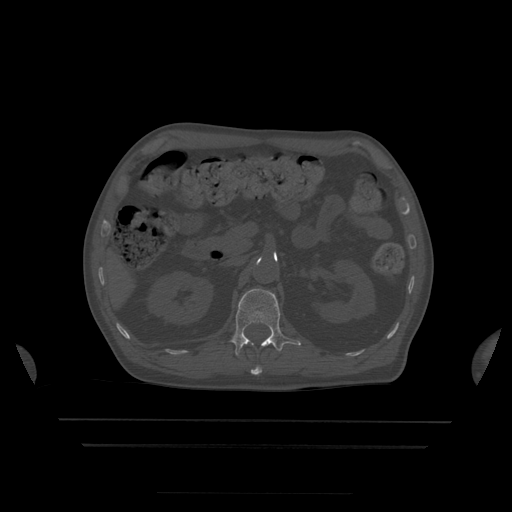
CT including the spine, one axial slice; position 174 of 522 along the scan axis; bone window (W 1800 / L 400 HU); 512 × 512 image matrix, field of view 436 × 436 mm. Patient age 68 years. From the clinical record (not read from this slice): primary cancer: urothelial.
Structures marked on this image (semi-automatically segmented with operator editing):
- L1 vertebra: bounding box (x1, y1, x2, y2) in pixels: (231, 289, 301, 356)
- T12 vertebra: (251, 367, 262, 375)